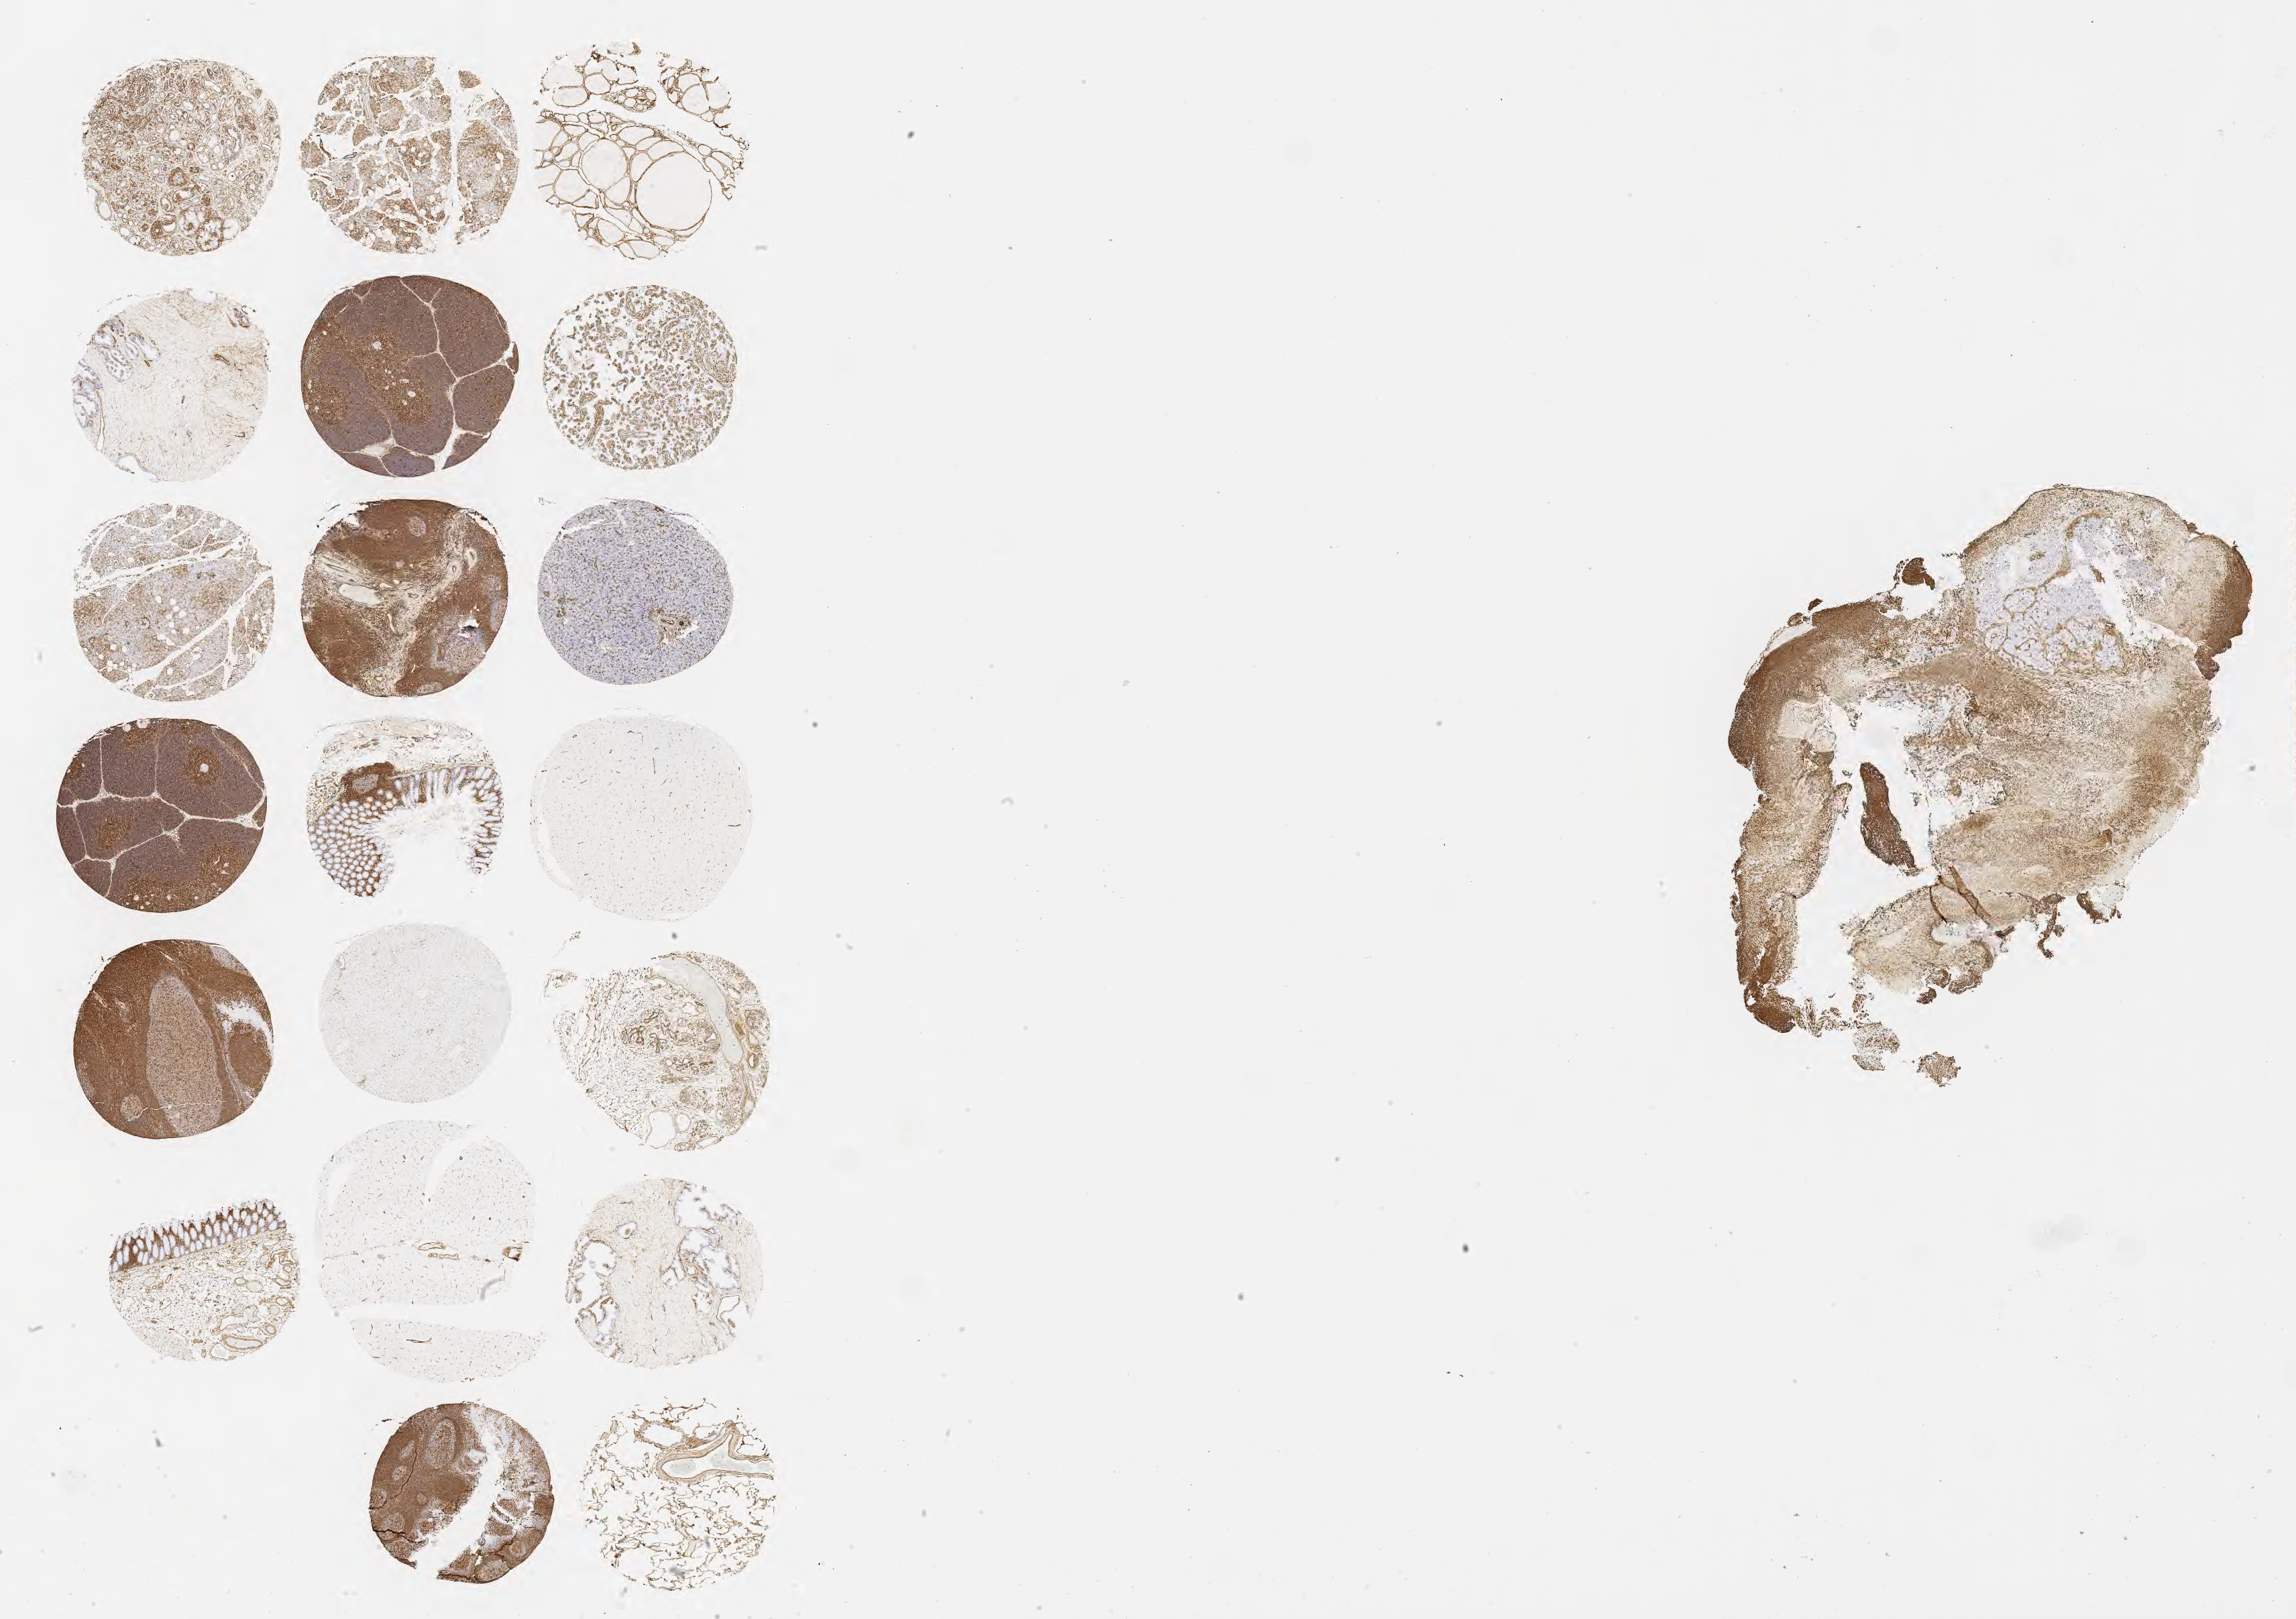
IHC for vimentin, whole-slide image — shown as a low-resolution overview of the whole scanned area (about 27.7 x 19.5 mm); specimen: tumor tissue; site: cervix. Female patient, age 62 years.
- histologic diagnosis: Squamous cell carcinoma, large cell, nonkeratinizing, NOS